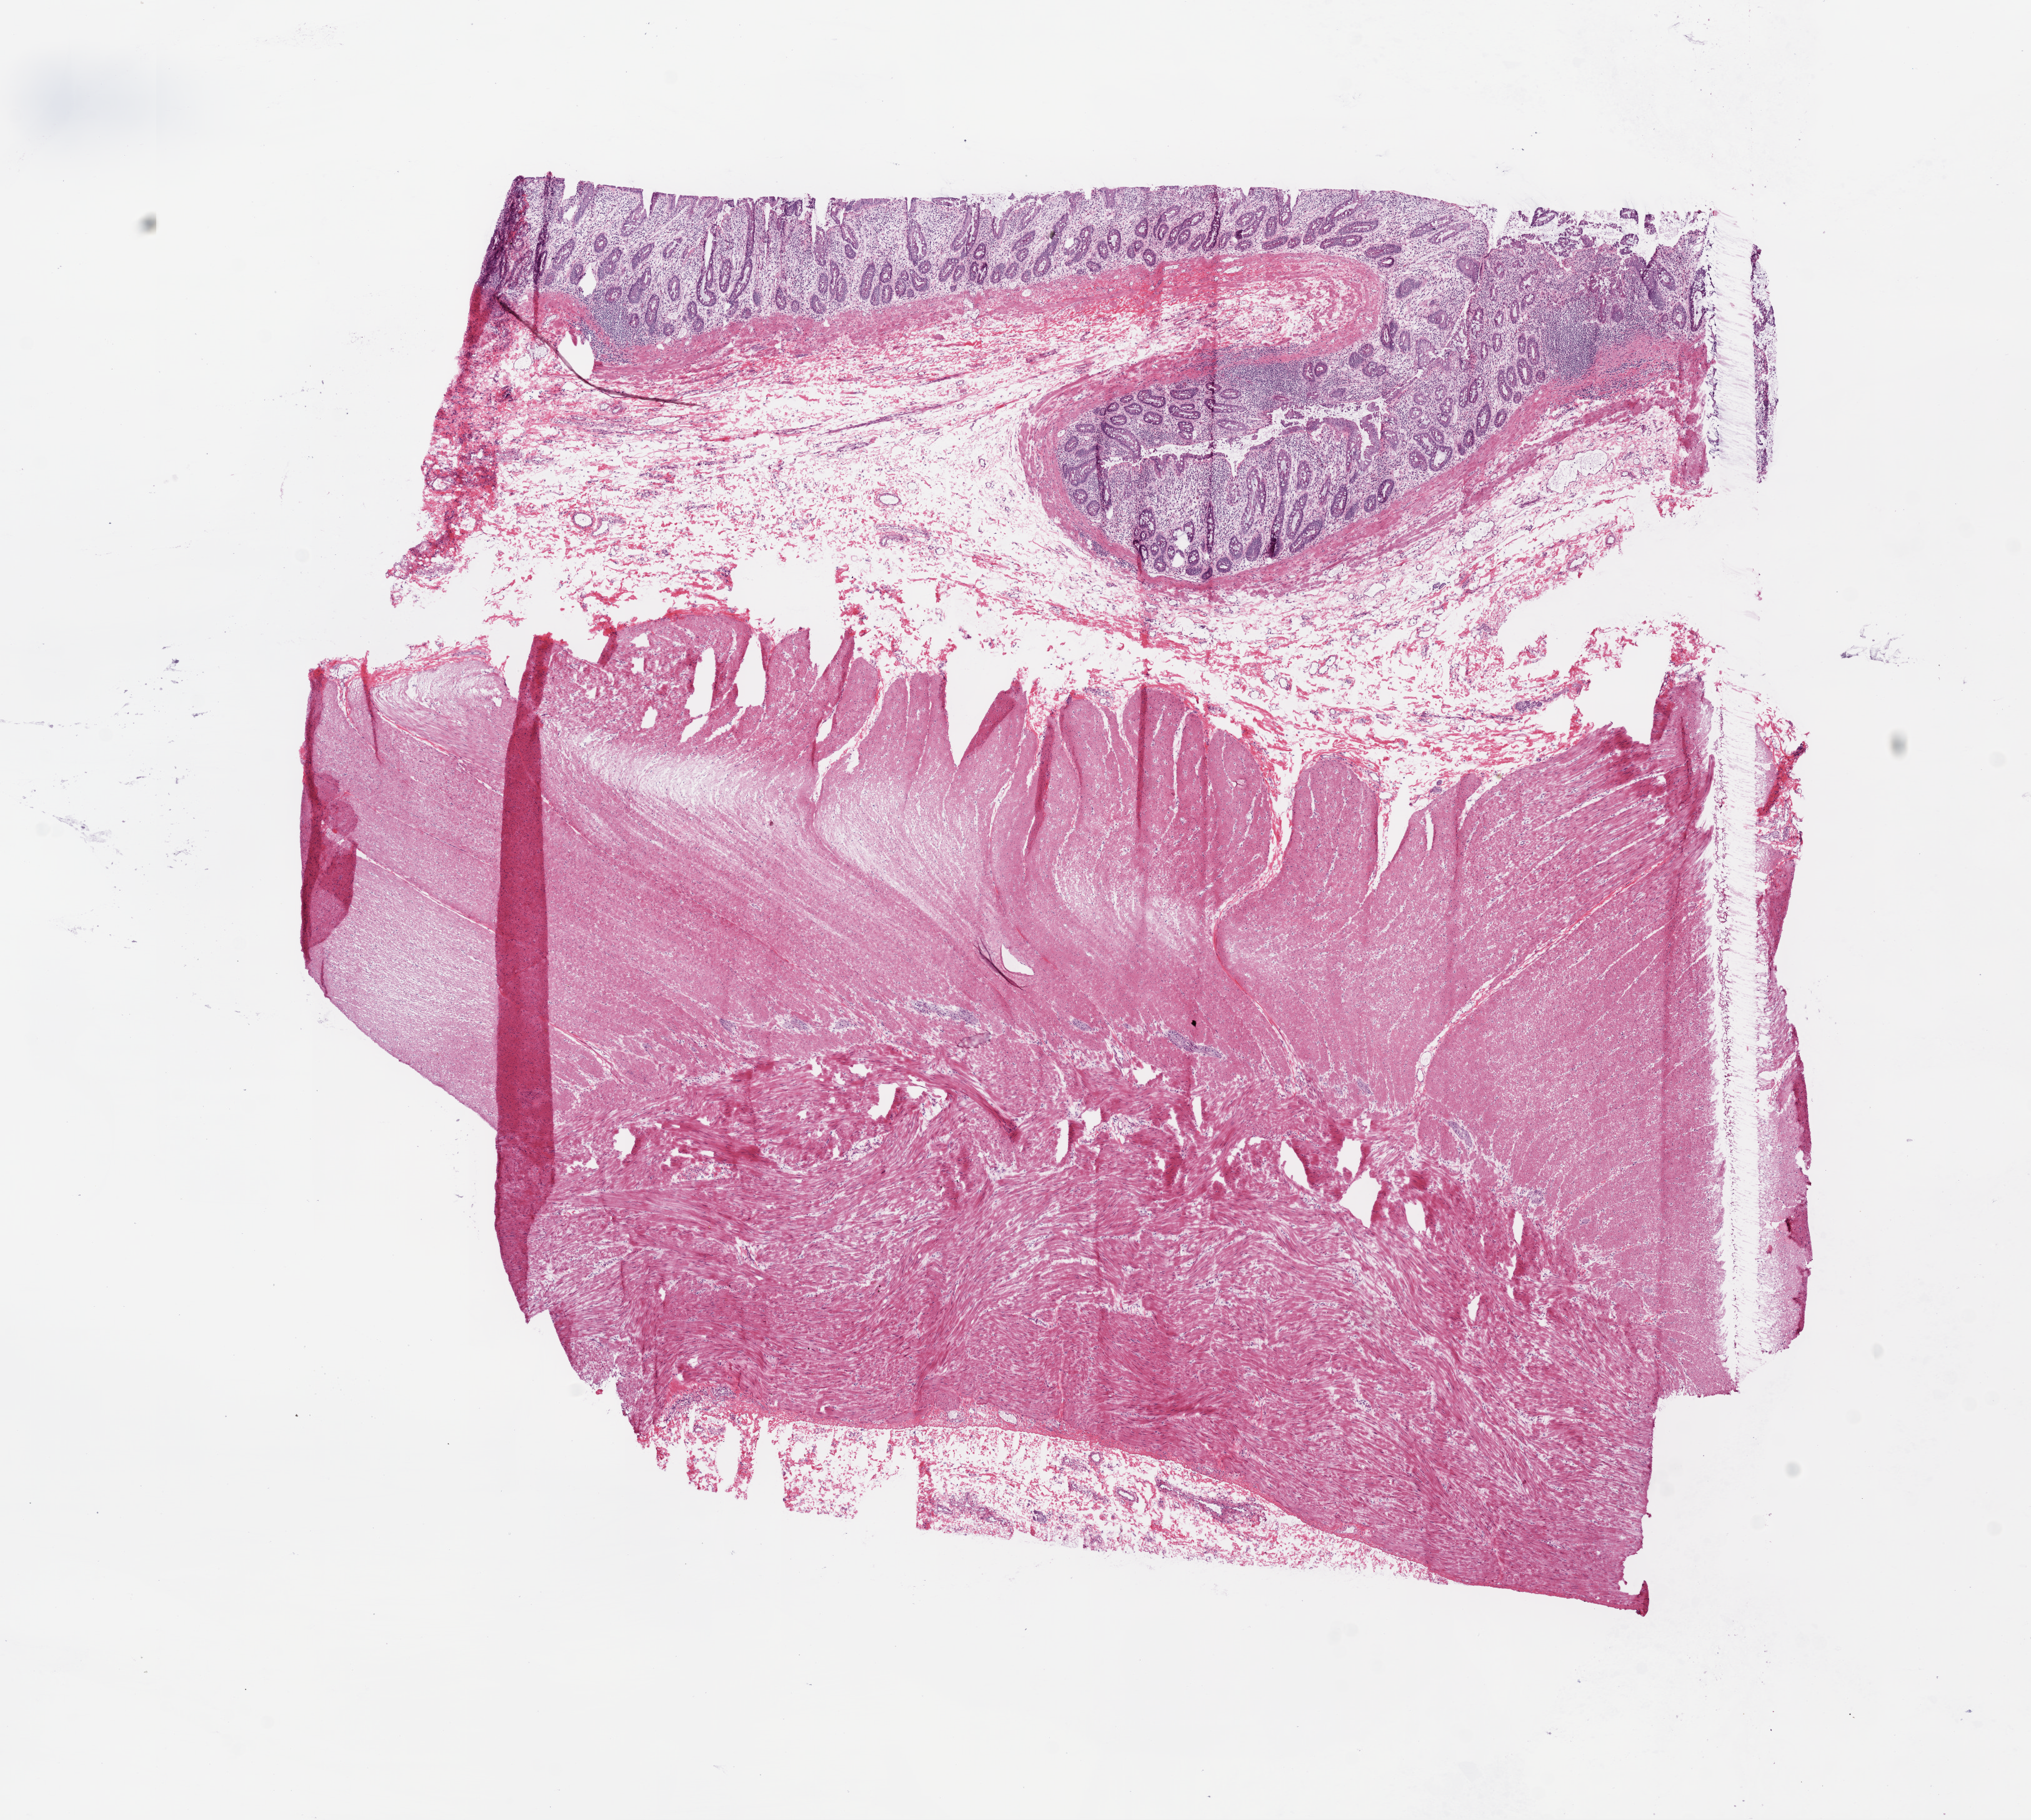
H&E-stained whole-slide image, whole scanned area (about 13.0 x 11.7 mm, from a 20x scan) shown as a low-resolution overview. Frozen section from the bottom of the tissue portion. Sample: solid tissue normal (non-tumour tissue), rectum. Male, age 39 years at initial diagnosis.
- this section: solid tissue normal (non-tumour) sample from the same patient
- patient diagnosis: Adenocarcinoma, NOS